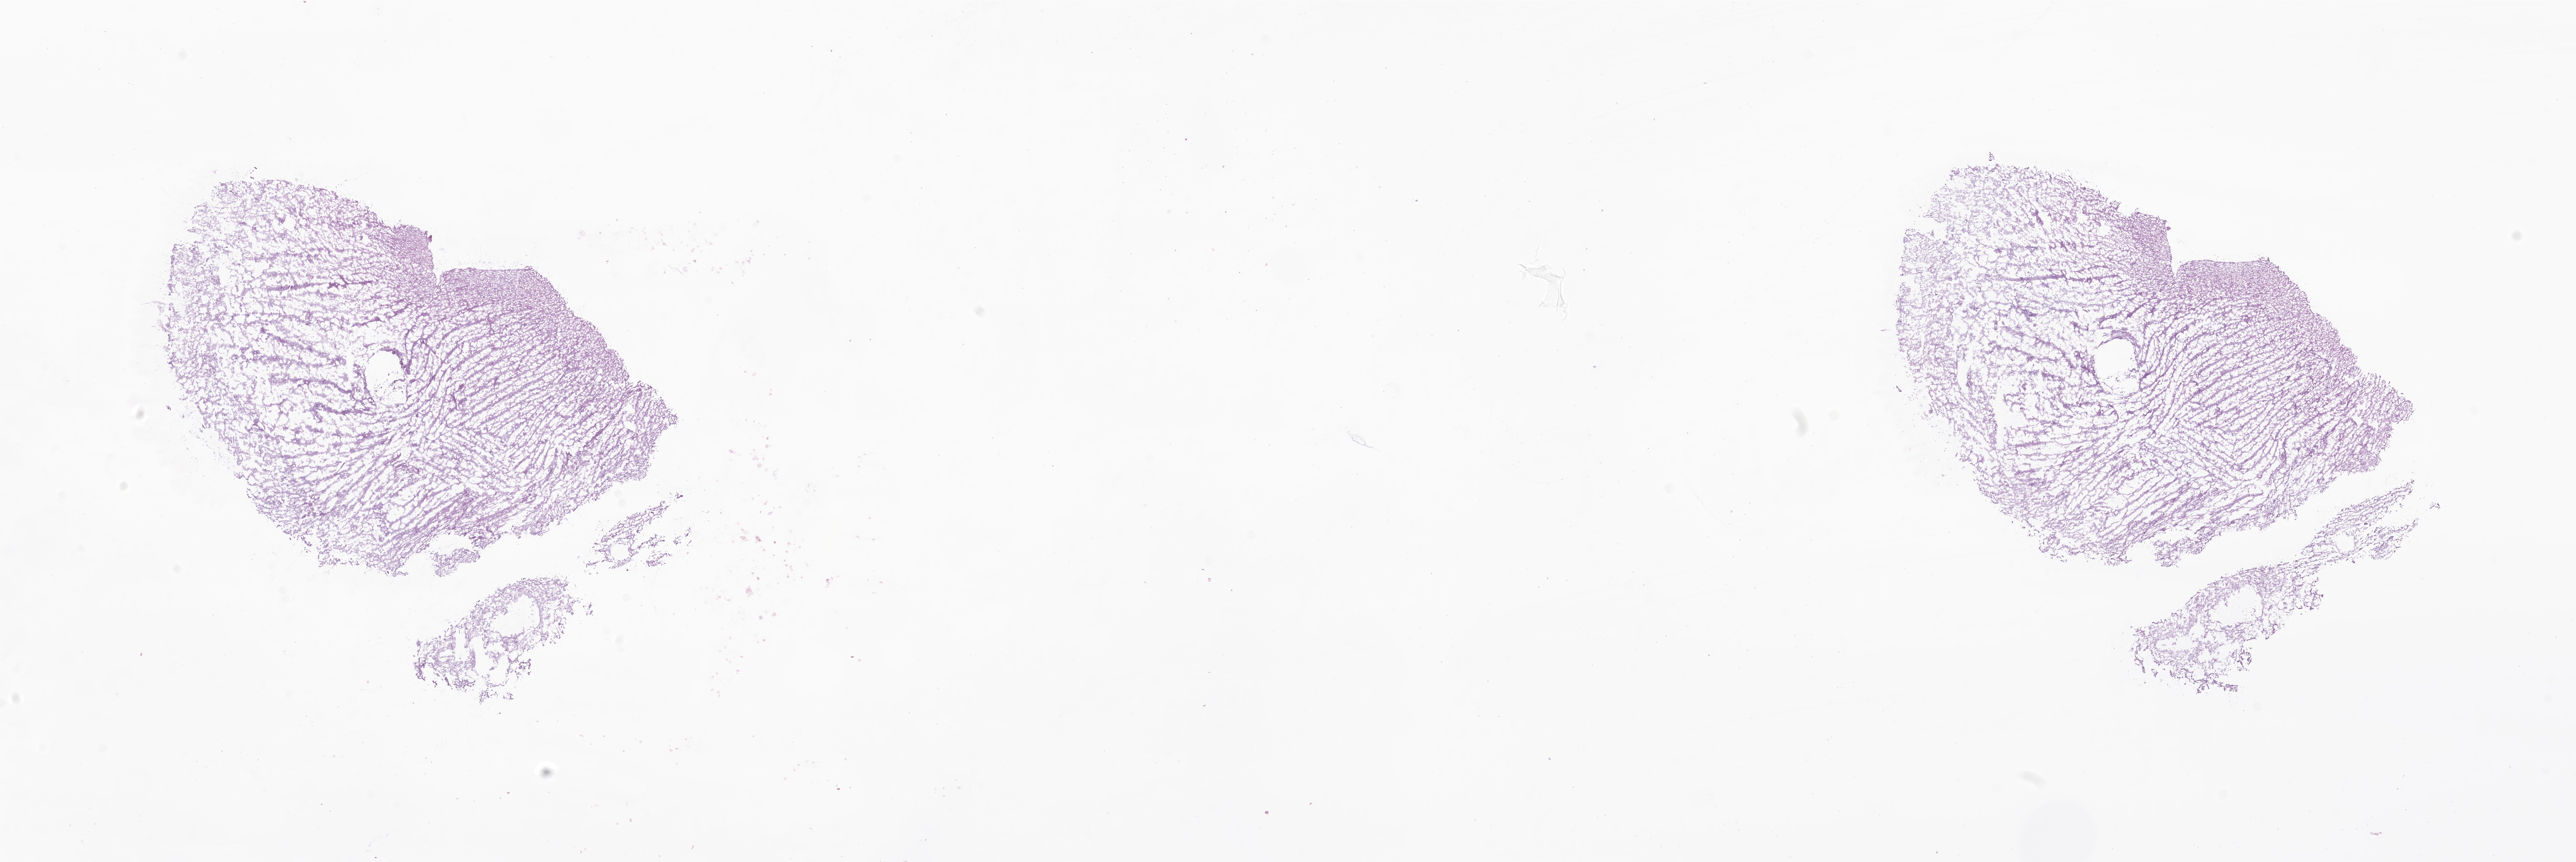
Digitized H&E-stained section of tumor tissue from the brain — whole scanned area (about 30.0 x 10.0 mm) shown as a low-resolution overview; frozen section. Patient: male, age 60 months (5 years).
Diagnosis: Pilocytic astrocytoma.